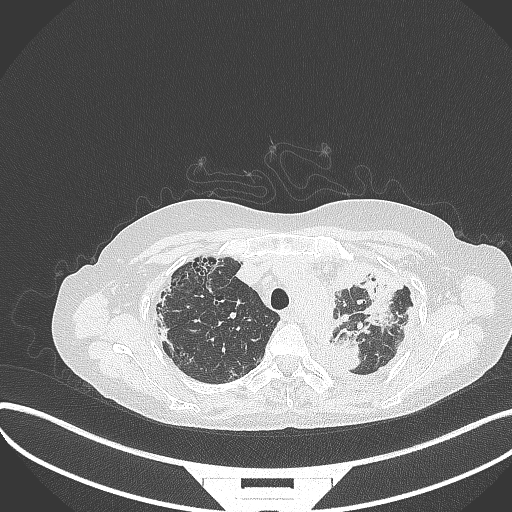
Chest CT, one axial slice; position 267 of 373 along the scan axis; reconstruction kernel B70f; 120 kVp; lung window (W 1500 / L -600 HU); 1 mm slice thickness; 512 × 512 image matrix, field of view 400 × 400 mm. Female patient, age 56 years. From the clinical record (not read from this slice): clinical TNM (as recorded): T1 N0 M0.
Annotated regions visible in this slice (bounding box drawn by a radiologist):
- lung tumour (recorded histology: adenocarcinoma): bounding box (x1, y1, x2, y2) in pixels: (326, 333, 368, 374)
- lung tumour (recorded histology: adenocarcinoma): (356, 255, 403, 331)